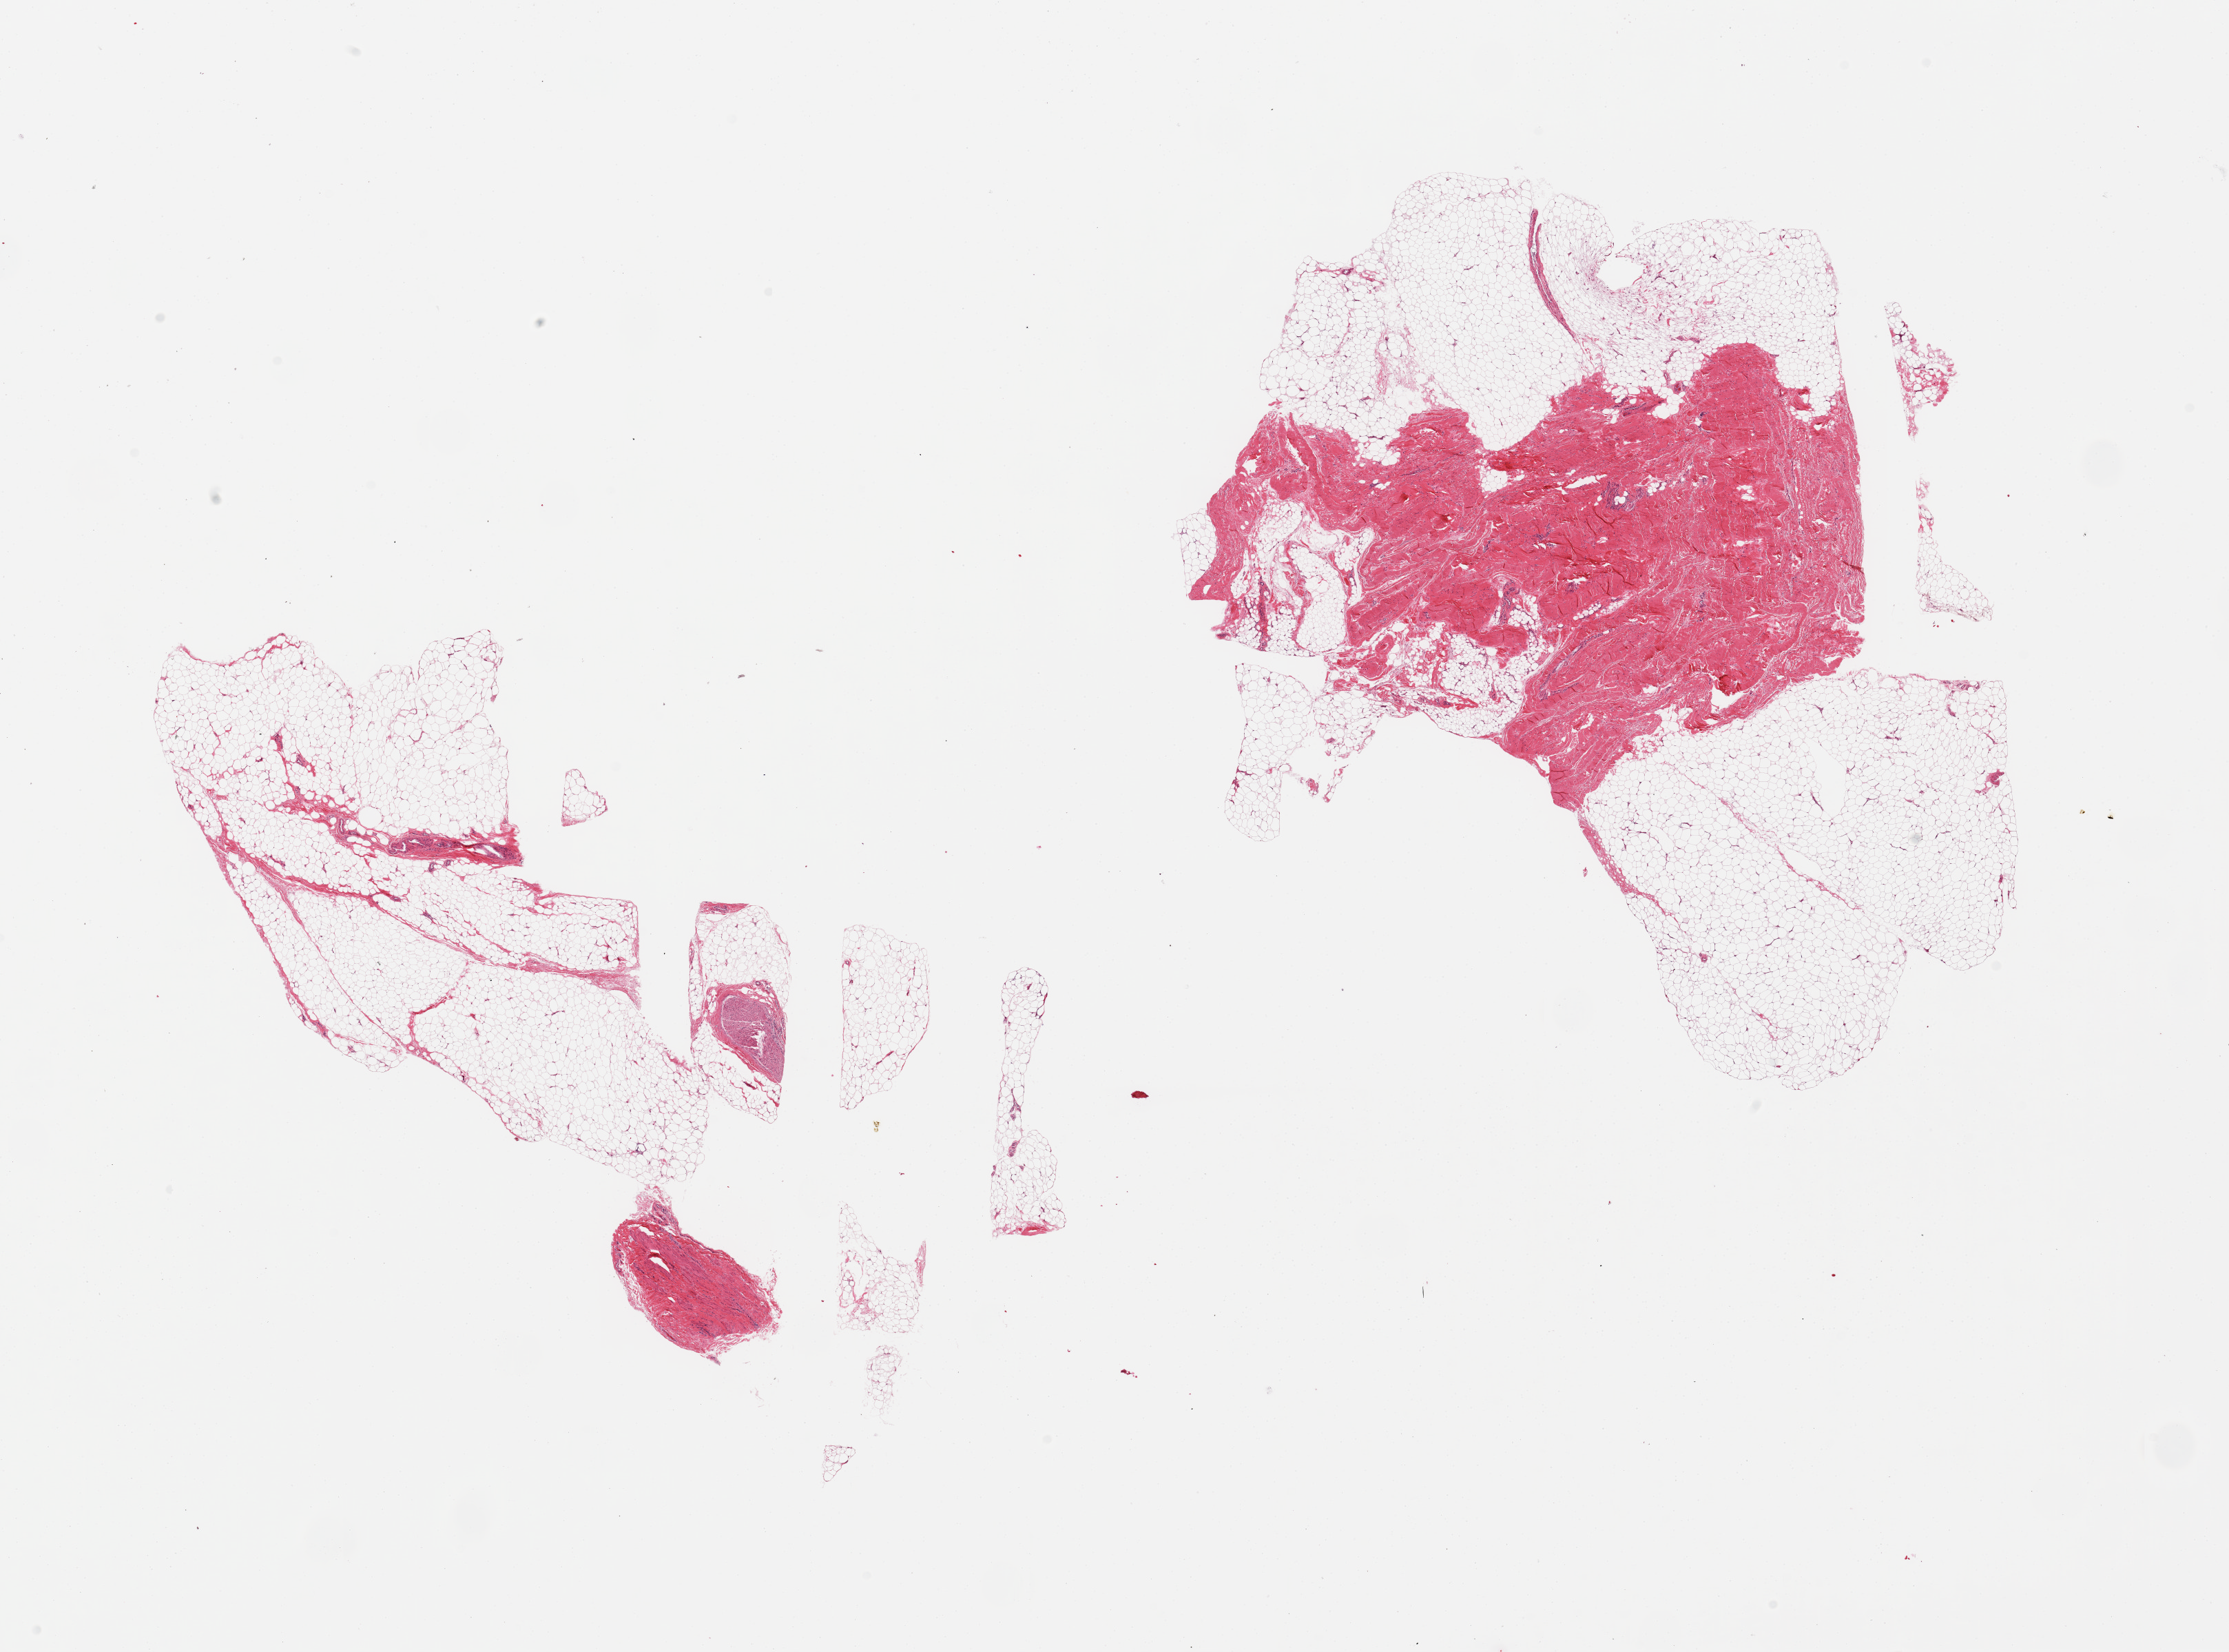
Haematoxylin and eosin whole-slide image, whole scanned area (about 25.6 x 19.0 mm, acquisition: 20x scan) shown as a low-resolution overview, PAXgene-fixed paraffin-embedded (PFPE) section, target tissue: adipose tissue, tissue donor sample.
Review note (as recorded): 2 pieces; 50% of 1 is fibrous tissue; 1mm nerve in other.